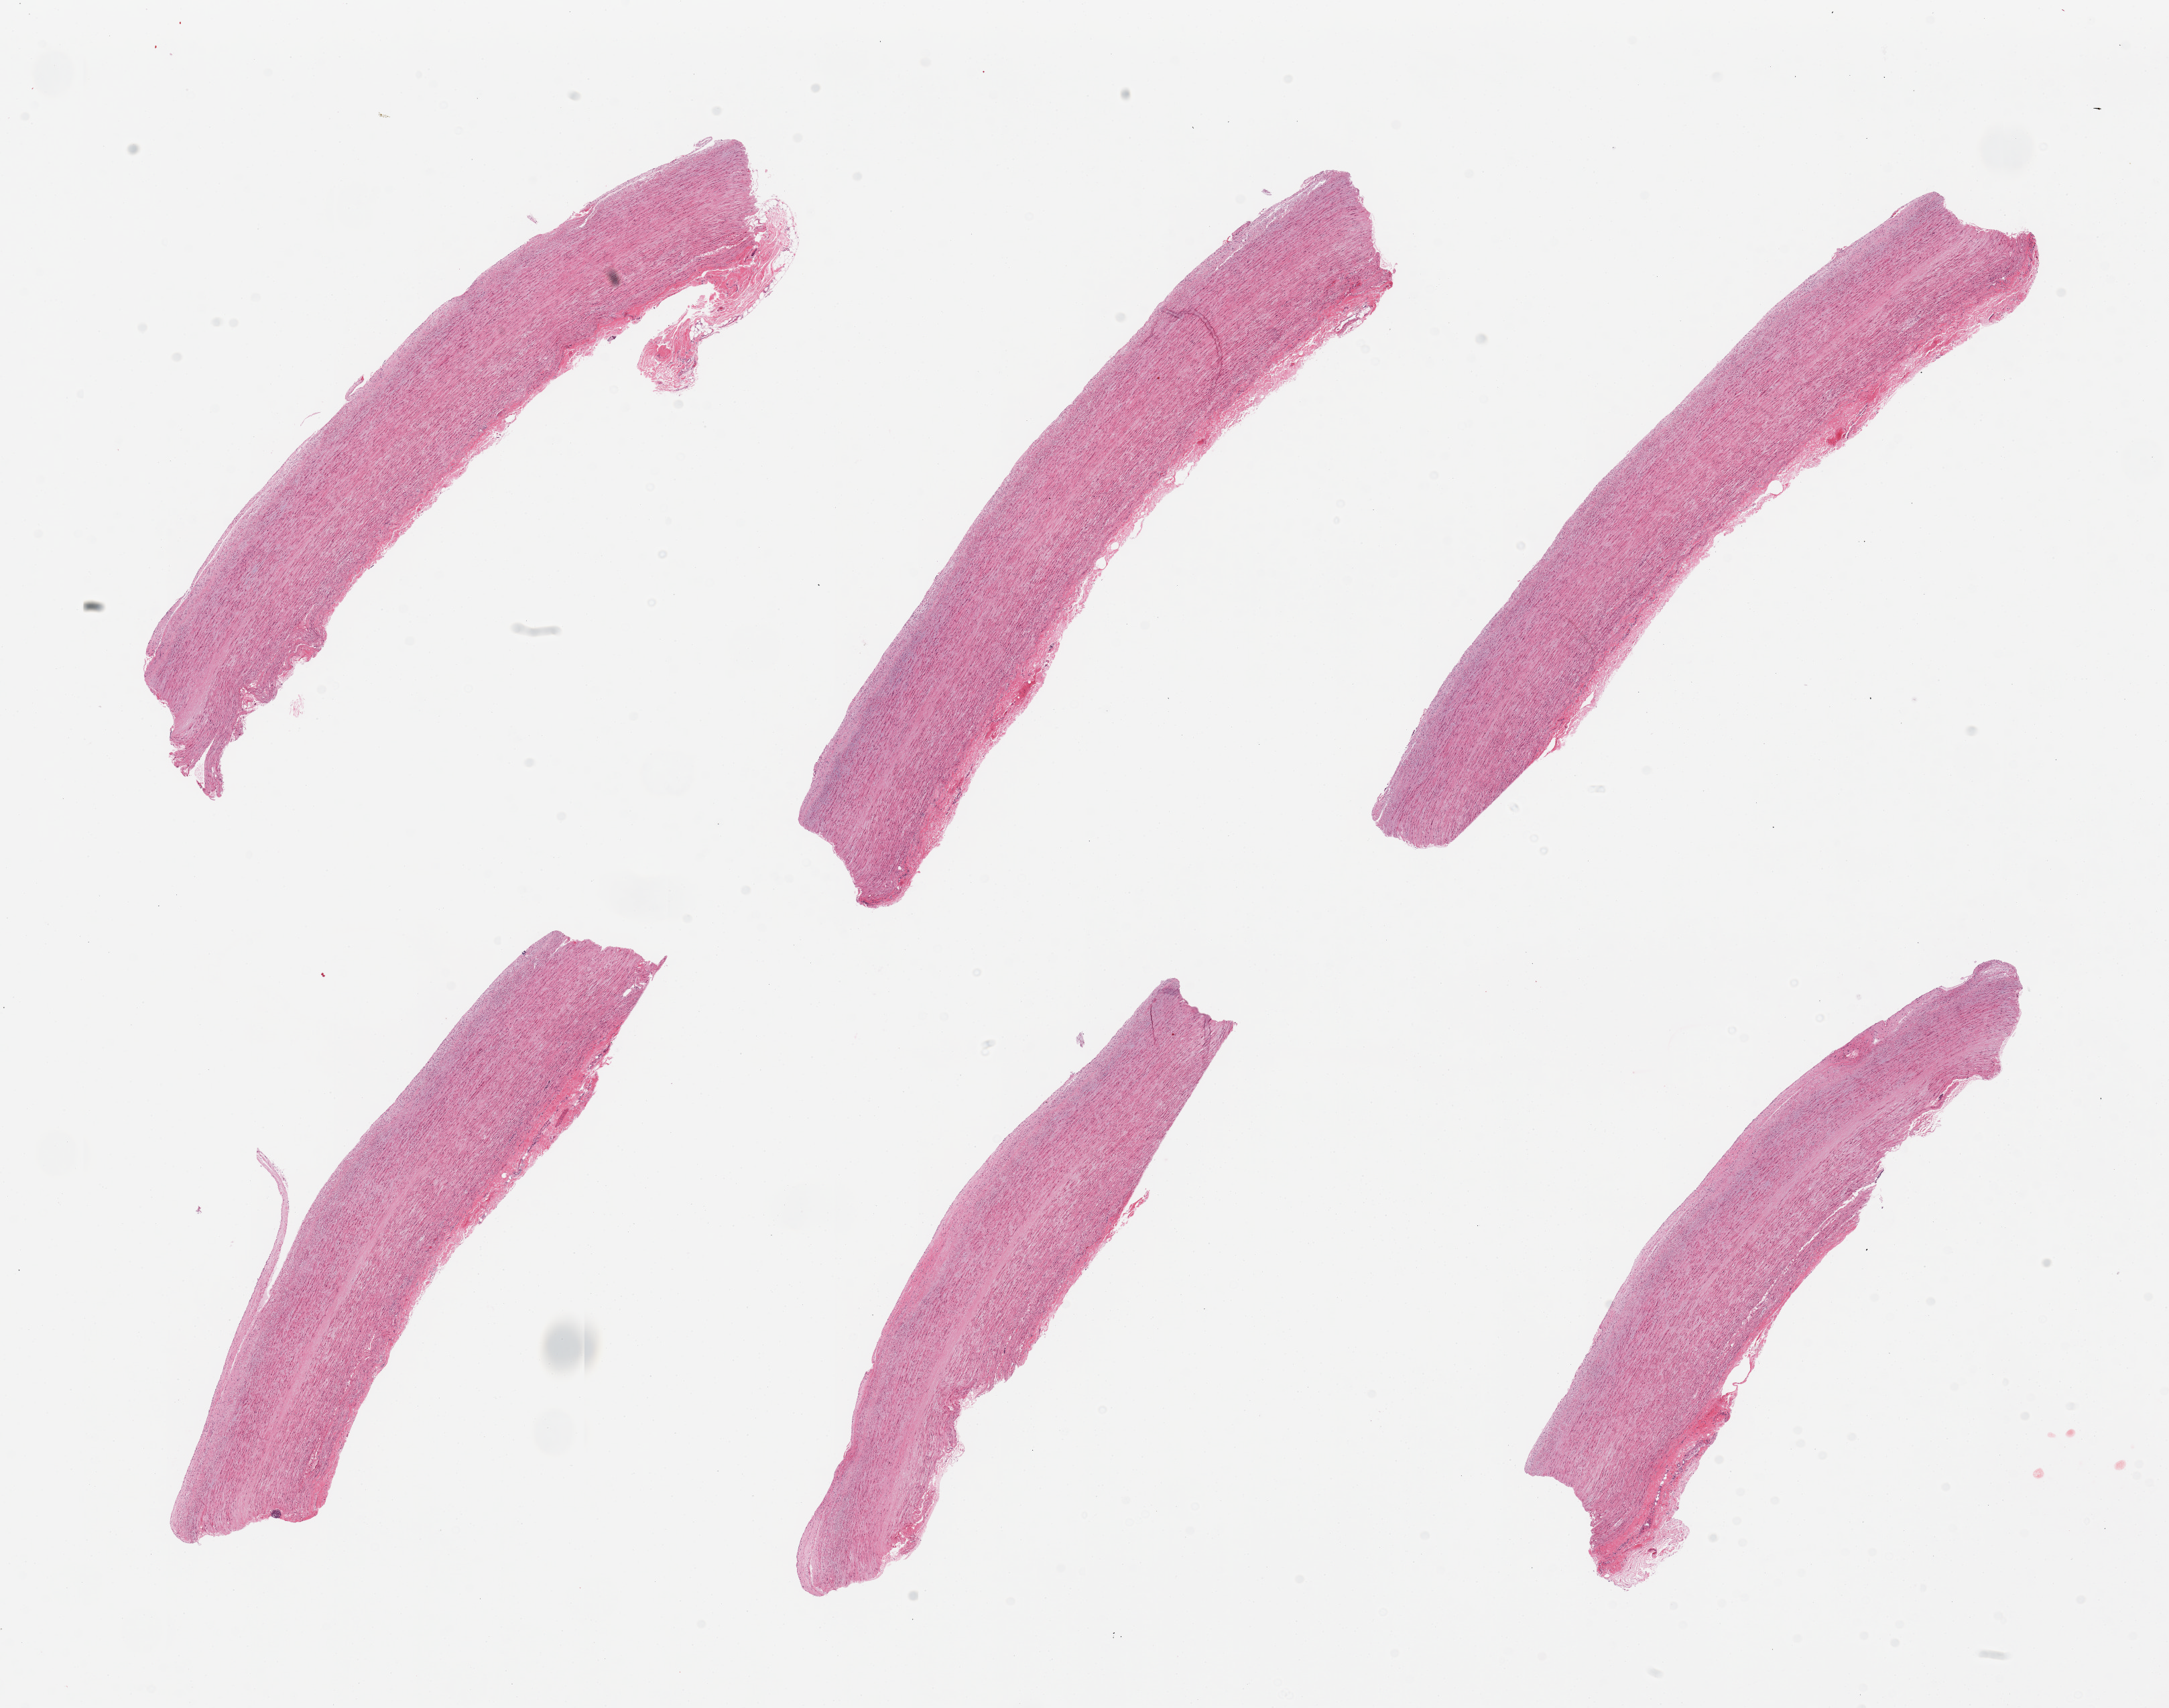
H&E whole-slide image — a low-resolution overview of the entire scanned area, about 25.6 x 20.2 mm (from a 20x scan), PAXgene-fixed paraffin-embedded (PFPE) section, section of aorta (target tissue), tissue donor sample. Donor sex: male.
Reviewer comment on this tissue sample: 6 pieces; no plaques; well trimmed.